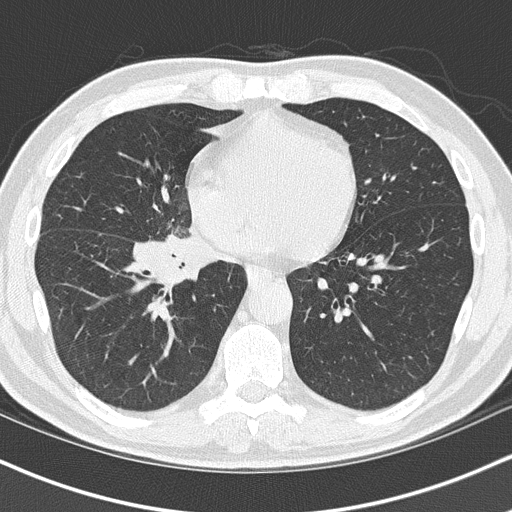
Chest CT (low-dose screening protocol), one axial image. Baseline screening round. Lung window (W 1500 / L -600 HU). 2 mm slice thickness. 512 × 512 image matrix. Male, age 55 years at enrolment. Current smoker at enrolment.
Lesion marked by an expert reader, bounding box (x1, y1, x2, y2) in pixels: (131, 226, 240, 308). Reader record for this screening exam (exam-level; its link to the box is not recorded): non-calcified nodule or mass ≥4 mm, right lower lobe, 6 × 5 mm, spiculated (stellate) margins, soft tissue attenuation. Official screen result: positive, change unspecified: nodule(s) >= 4 mm or enlarging nodule(s), mass(es), or other non-specific abnormalities suspicious for lung cancer. Lung cancer was diagnosed 21 days after this screen: carcinoma, NOS, right hilum, stage IB (AJCC 6th edition), 67 mm at pathology.